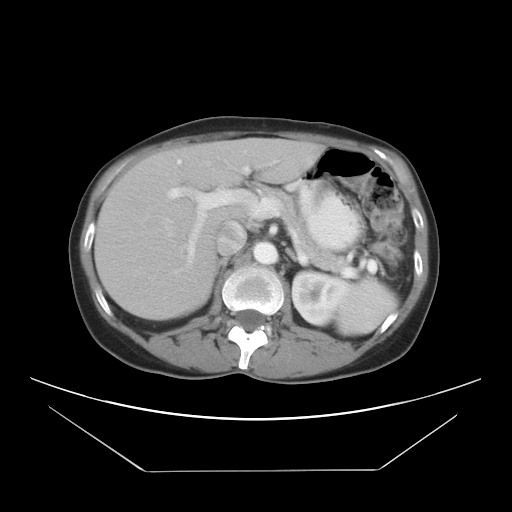
Contrast-enhanced abdominal CT, one axial slice; slice 17 of 30 in the series (ordered by position); 120 kVp; intravenous contrast given; soft-tissue window (W 400 / L 40 HU); 512 × 512 image matrix, field of view 412 × 412 mm. Female patient, age 54 years. Case-level facts recorded for this patient, not image findings: diagnosis: colorectal cancer liver metastases, imaged before liver resection; multiple liver metastases: yes; largest metastasis: 2.5 cm; disease in both lobes: yes.
Outlined on this slice (manually delineated by an expert):
- hepatic veins: box from (x=156, y=232) to (x=173, y=300) px
- liver: (x=96, y=140)–(x=320, y=321)
- planned liver remnant (the part of the liver to remain after resection): (x=100, y=141)–(x=248, y=321)
- portal vein (with intrahepatic branches): (x=166, y=158)–(x=248, y=273)